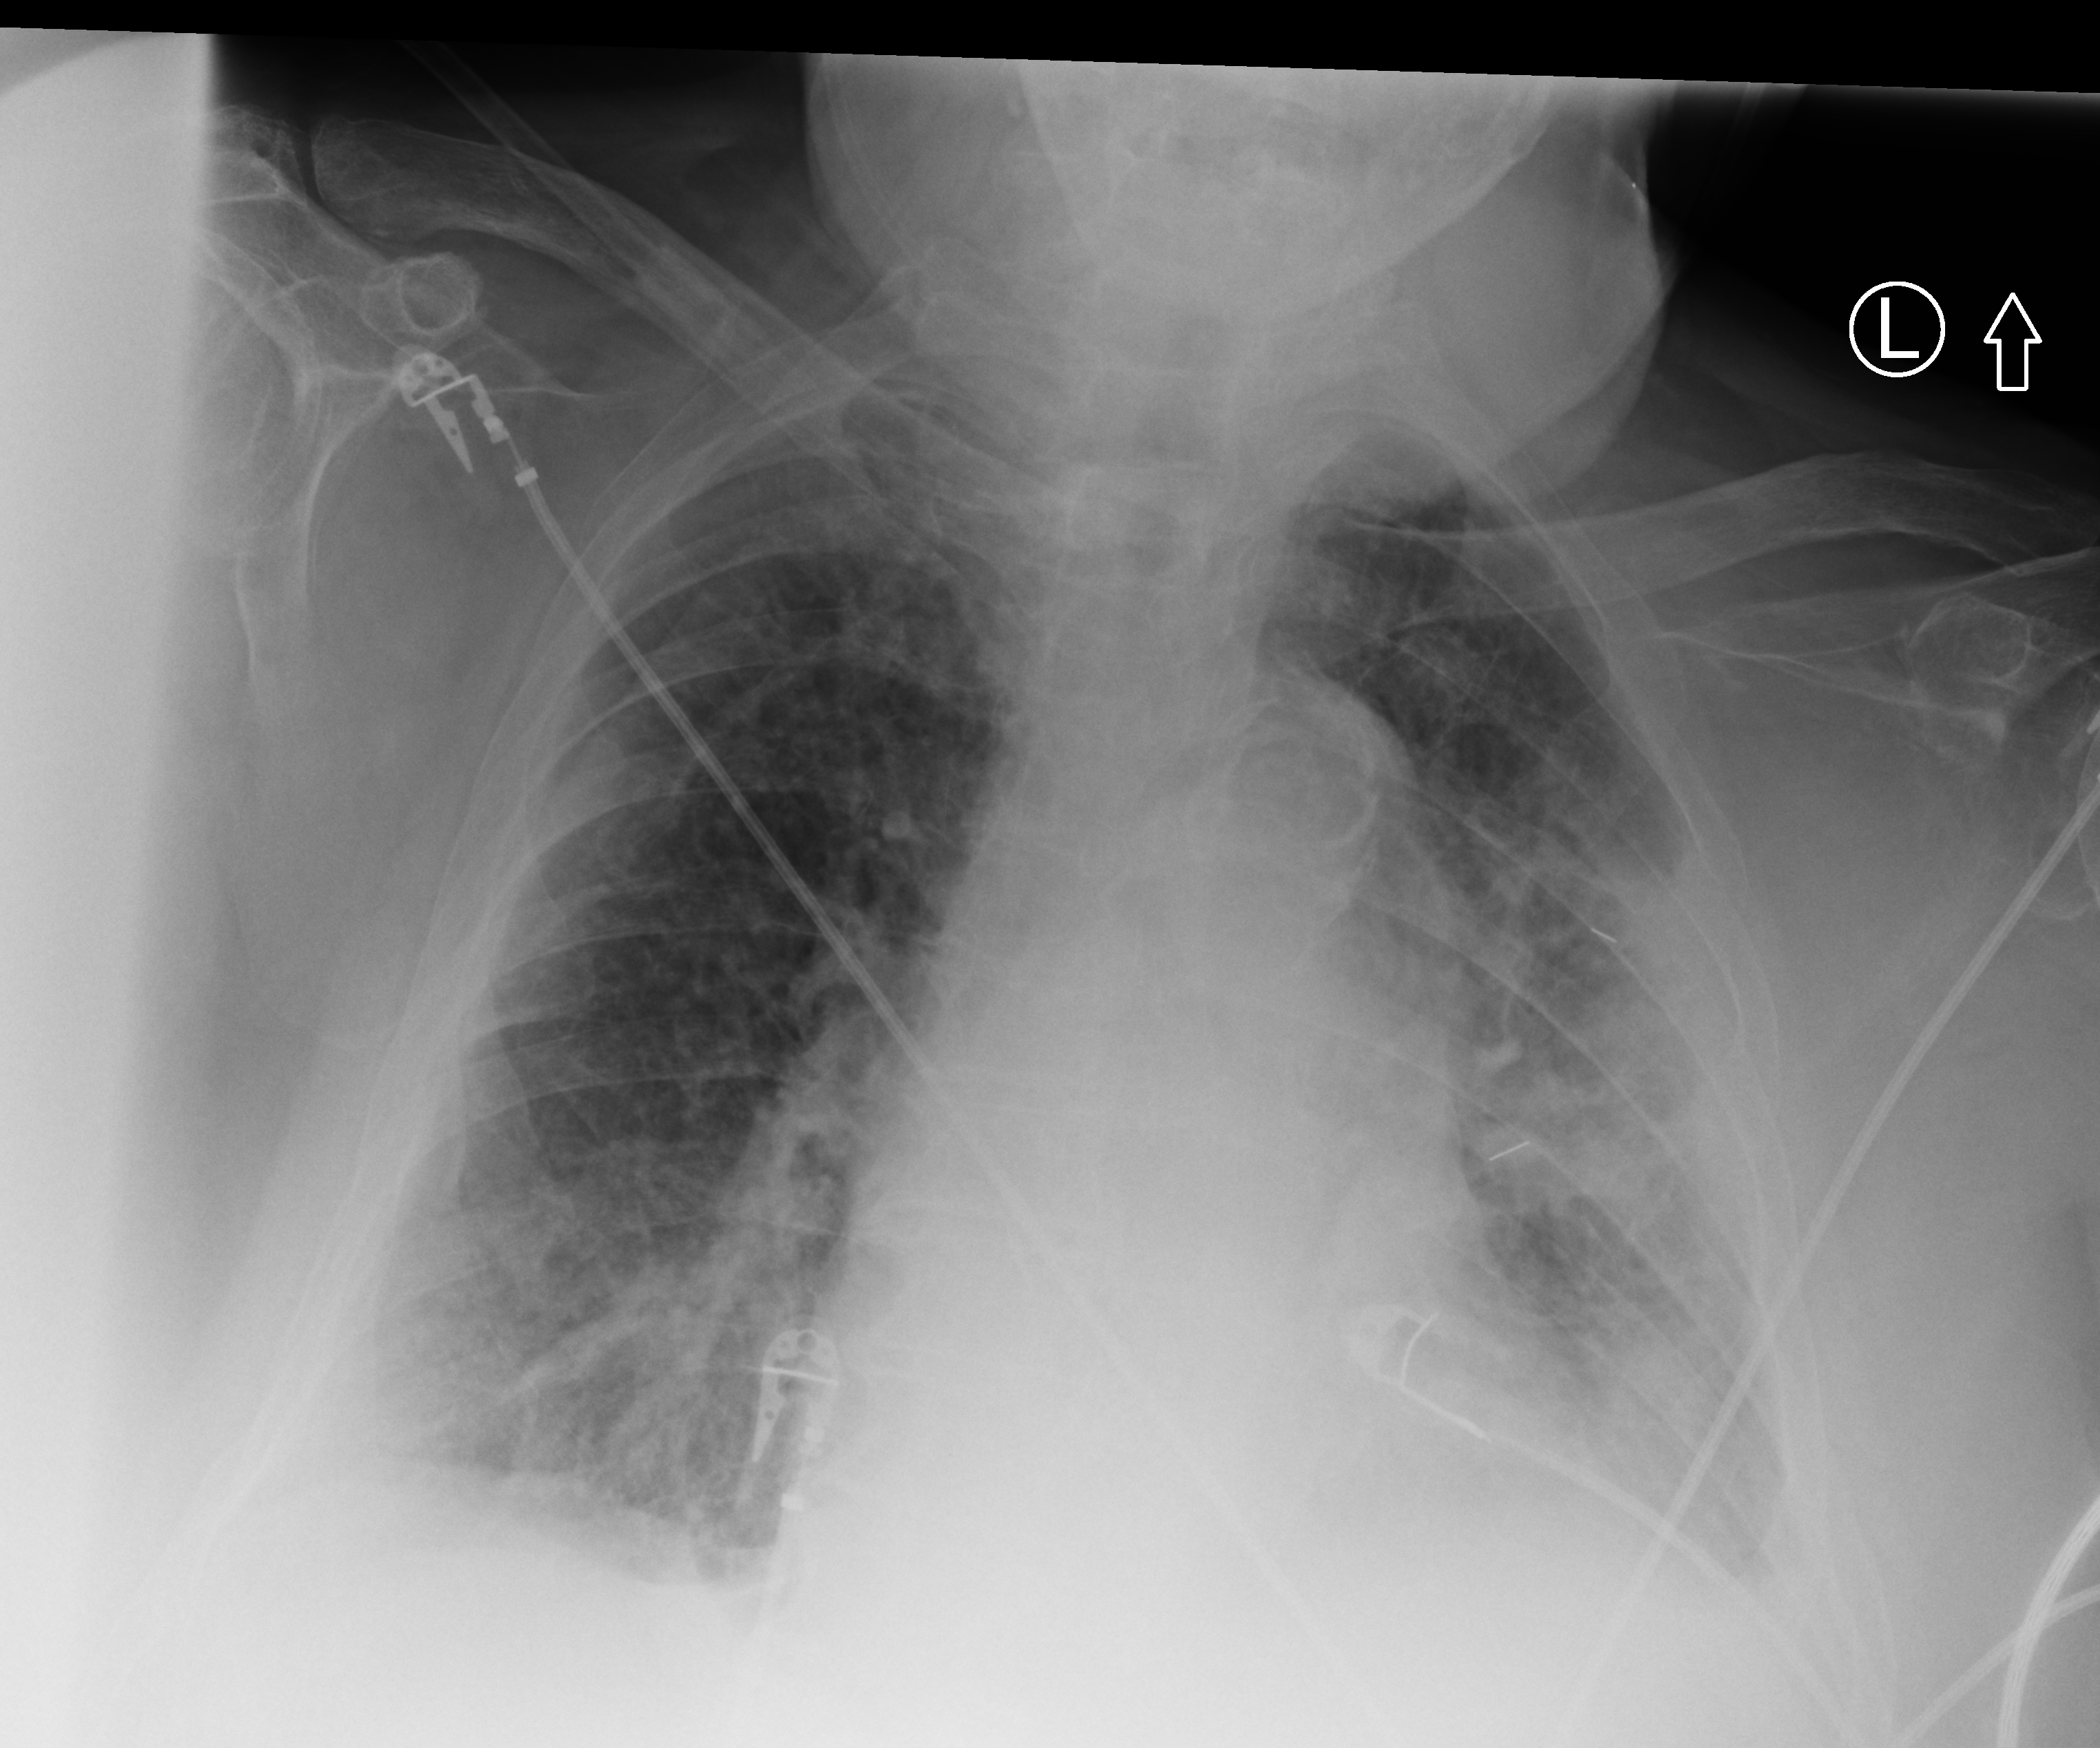
Portable chest radiograph, anteroposterior (AP) projection. Patient hospitalised with COVID-19; male, aged 75–90 years.
From the hospital-stay record, not from the radiograph (when in the stay this image was taken is not recorded):
- admitted to intensive care during this hospital stay: no
- smoking status (admission record): former
- mechanically ventilated during this hospital stay: no